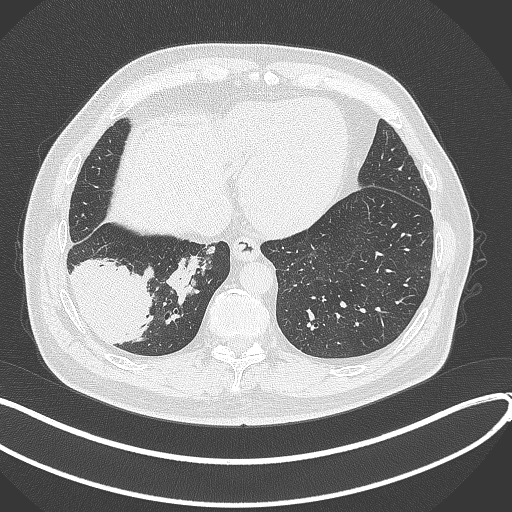
Chest CT, one axial slice. Slice 86 of 360 in the series (ordered by position). Reconstruction kernel B70f. 120 kVp. Lung window (W 1500 / L -600 HU). 512 × 512 image matrix, field of view 400 × 400 mm. Patient: male, 59 years.
Outlined on this slice (rectangle marked by the reading radiologist):
- lung tumour (recorded histology: adenocarcinoma): bounding box [x1, y1, x2, y2] px = [70, 248, 155, 347]